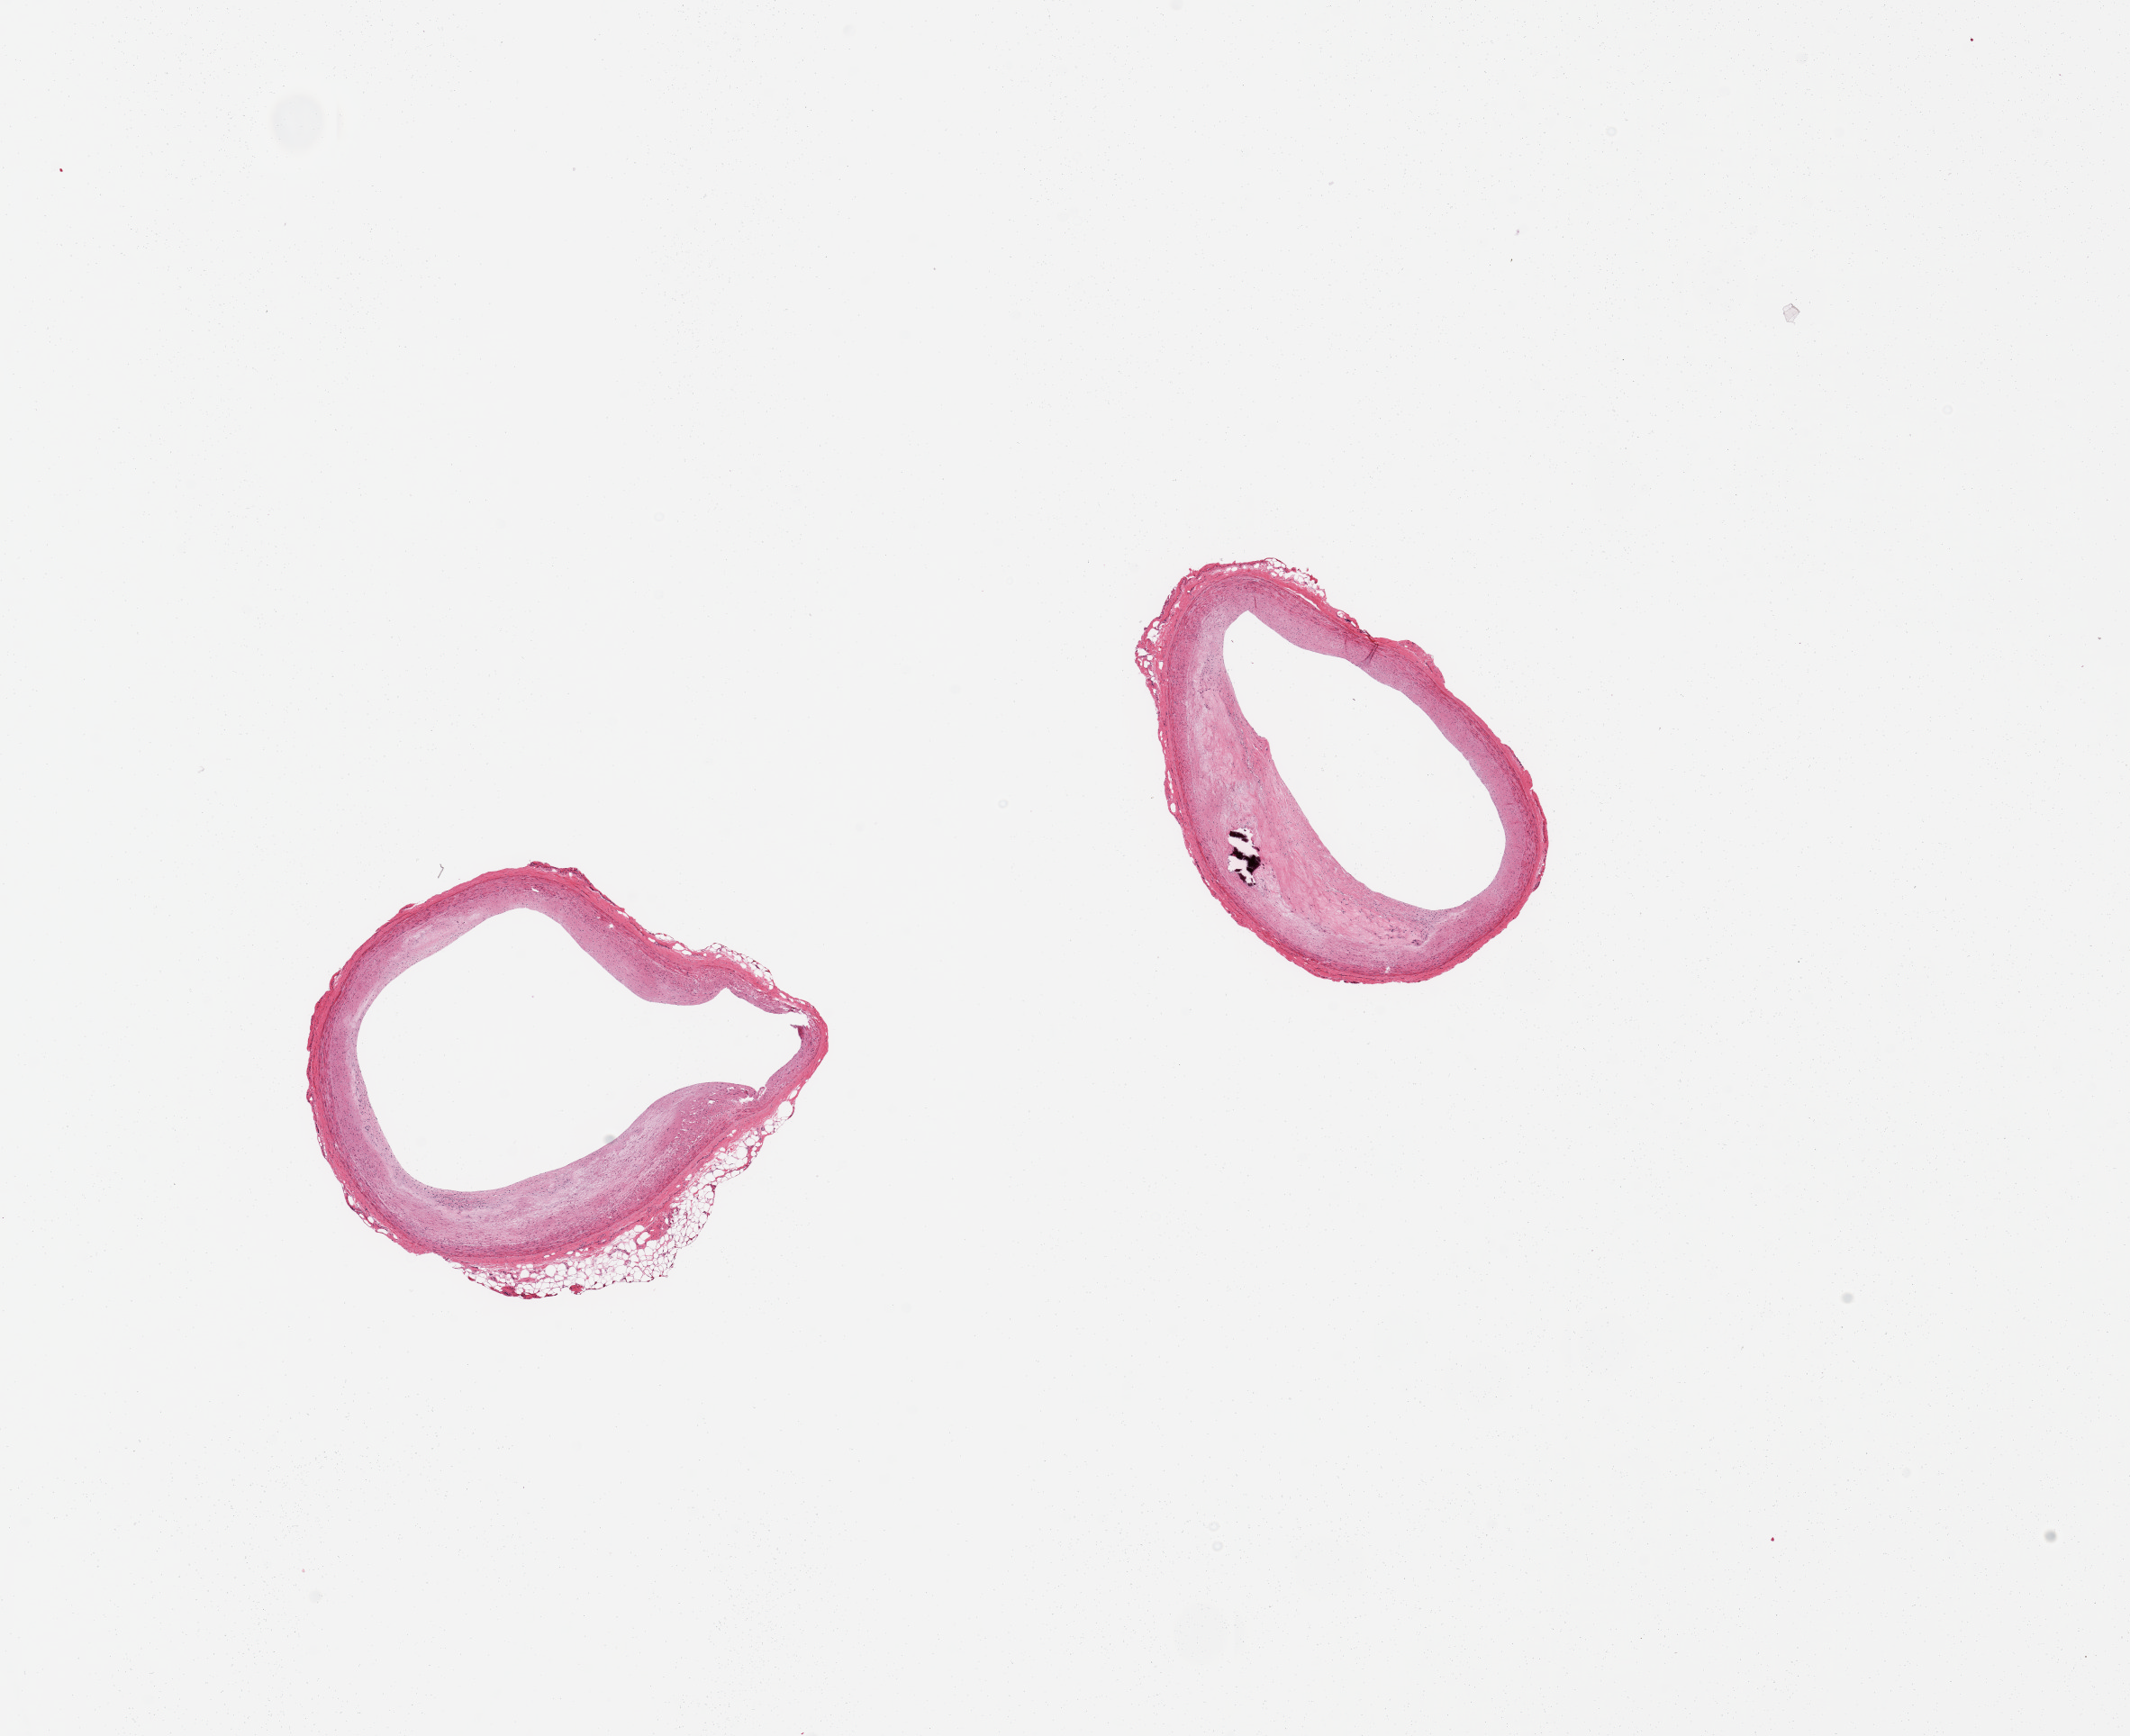
Haematoxylin and eosin whole-slide image — low-resolution overview of the scanned area, about 18.7 x 15.2 mm, PAXgene-fixed paraffin-embedded (PFPE) section, target tissue: coronary artery, tissue donor sample. Donor sex: male.
Pathologist's review note for this sample: 2 pieces, moderate atherosis, focally calcified, ~40-50% luminal occlusion.